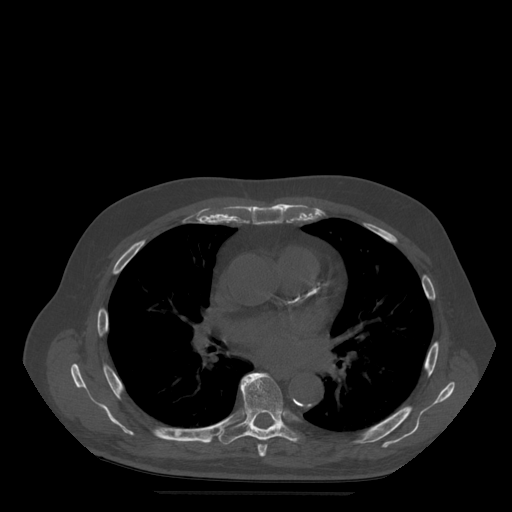
CT including the spine, one axial slice. Position 337 of 522 along the scan axis. Bone window (W 1800 / L 400 HU). 1.25 mm slice thickness. 512 × 512 image matrix, field of view 420 × 420 mm. Patient age 72 years. From the clinical record (not read from this slice): primary cancer: prostate.
Outlined on this slice (semi-automatic segmentation, software-assisted and operator-edited):
- T6 vertebra: box from (x=242, y=384) to (x=268, y=457) px
- T7 vertebra: (x=217, y=373)–(x=305, y=445)